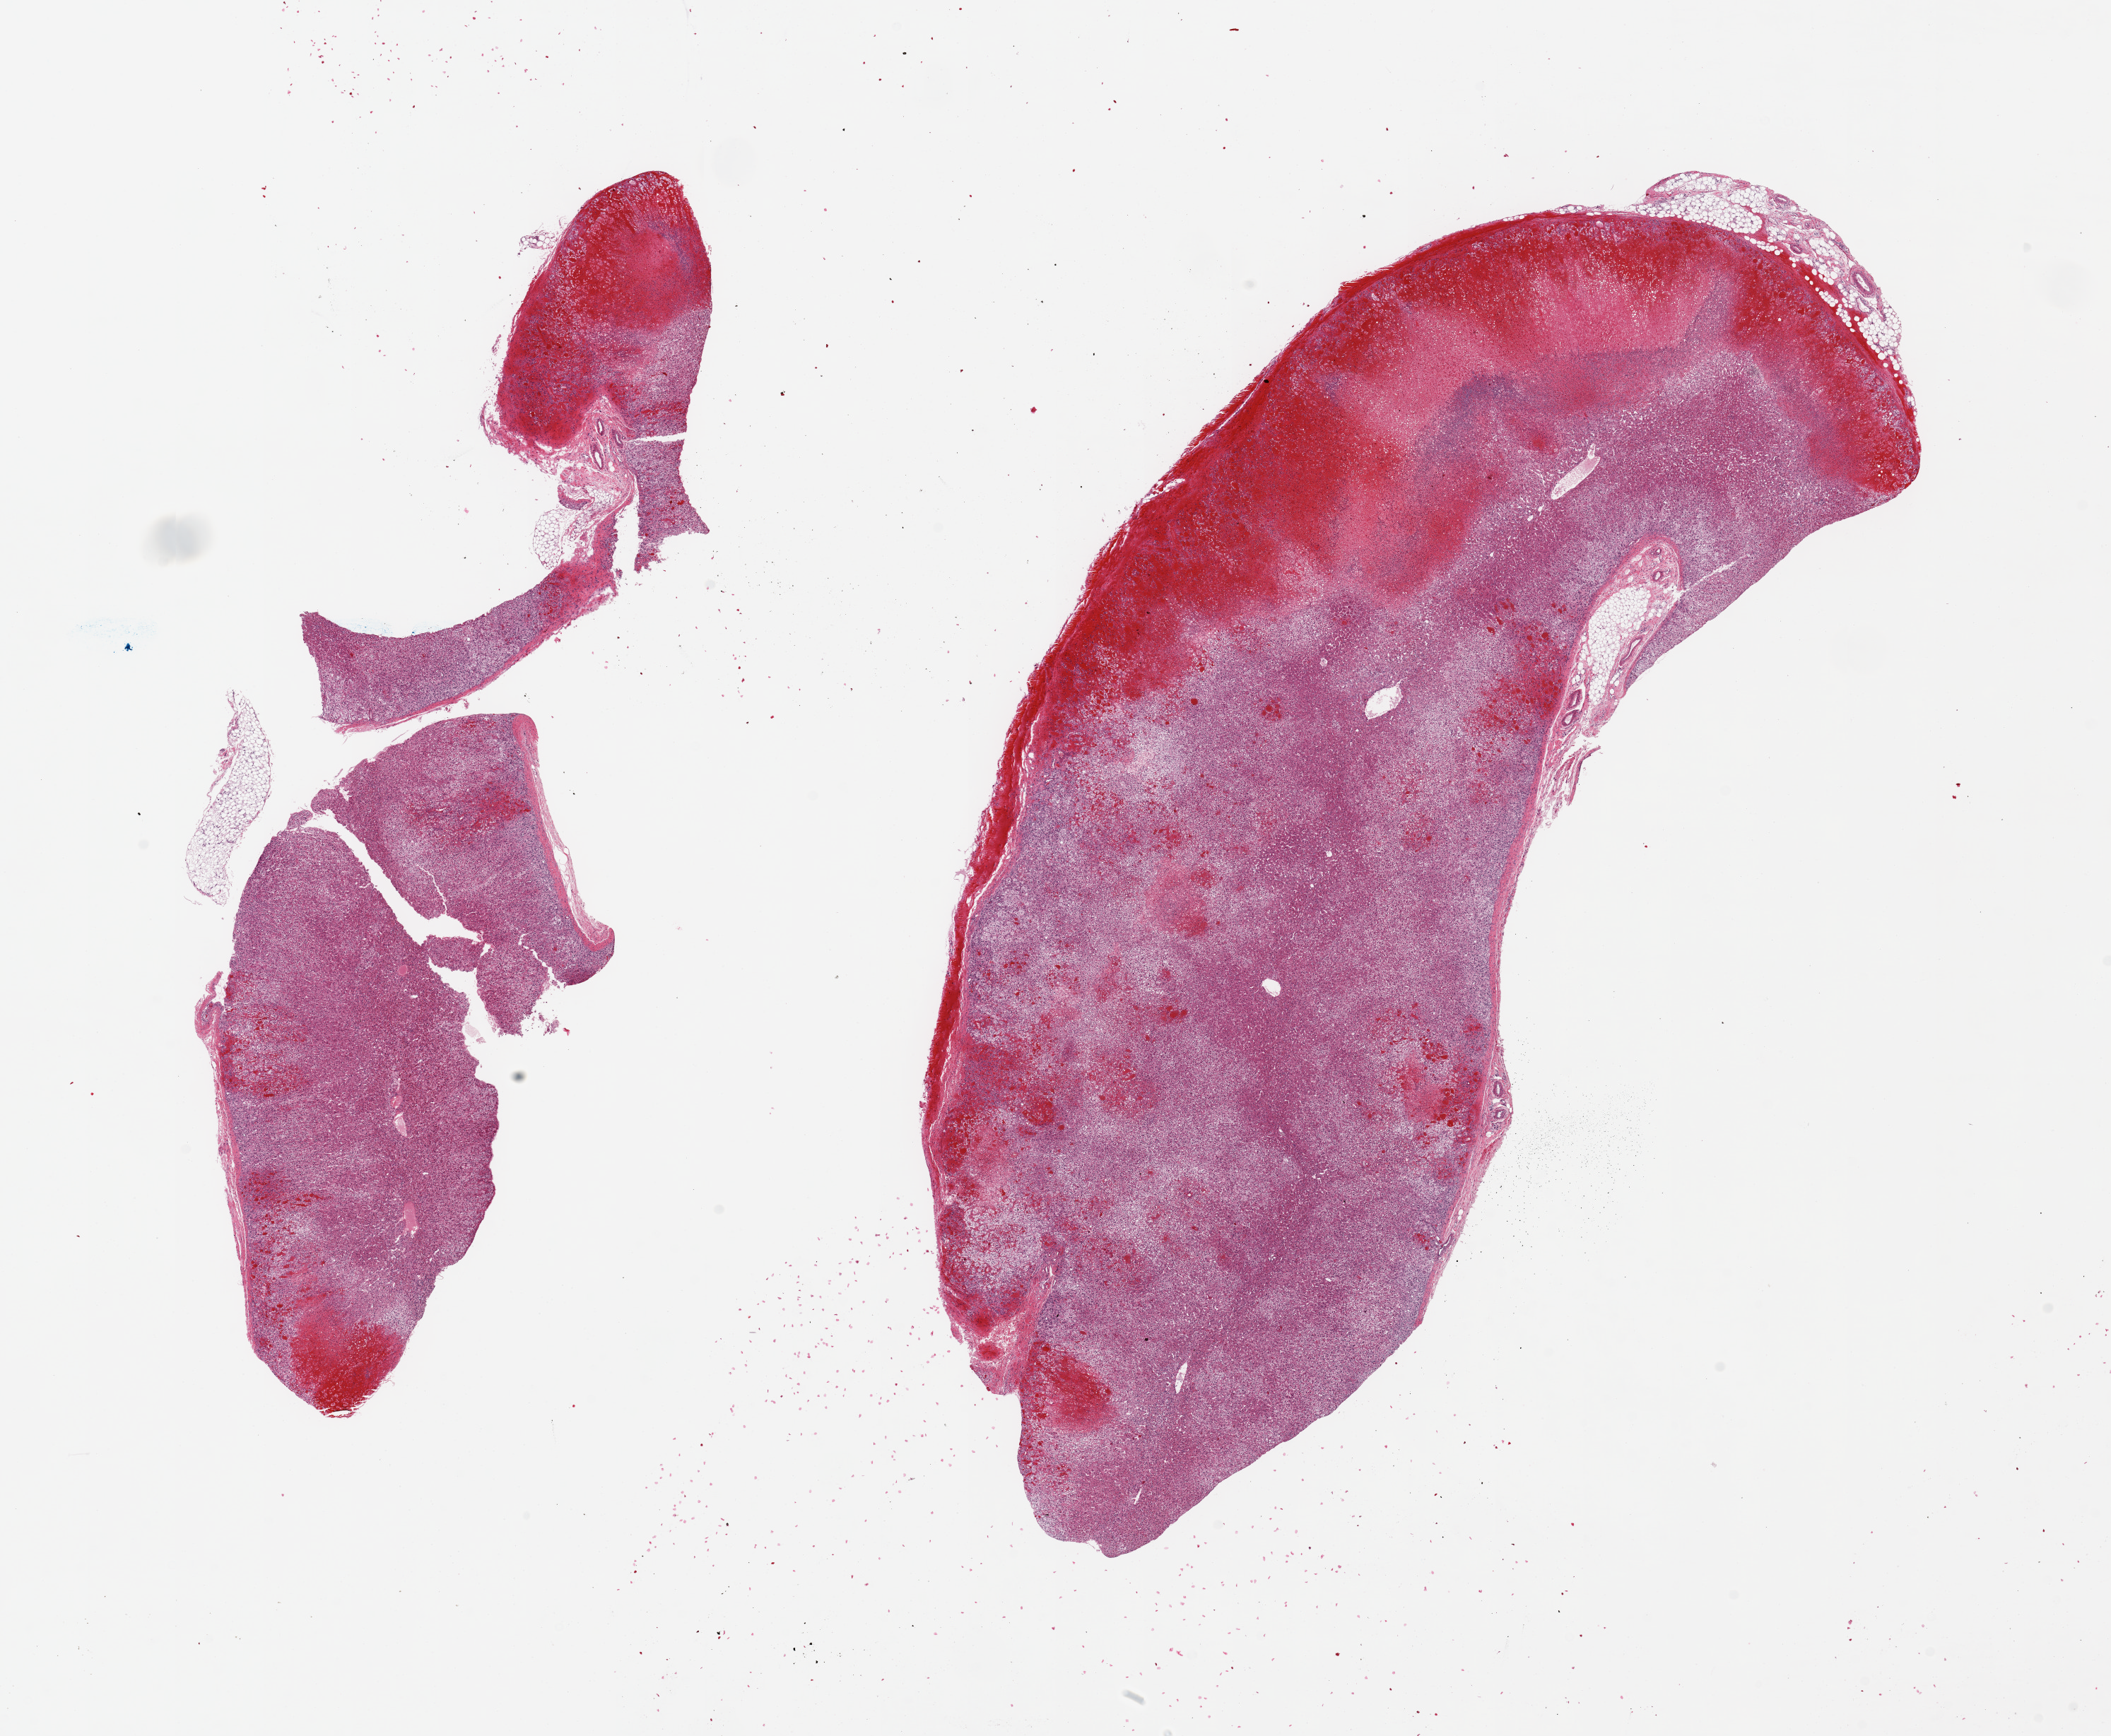
Digitized hematoxylin and eosin (H&E)-stained section, brightfield — low-resolution overview of the scanned area, about 23.6 x 19.4 mm; PAXgene-fixed paraffin-embedded (PFPE) section; section of adrenal gland (target tissue); tissue donor sample. Female donor.
• review note (as recorded): 2 pieces, 14x5 & 17x7mm; patchy hemorrhagic infarction, all cortex, infarcted areas